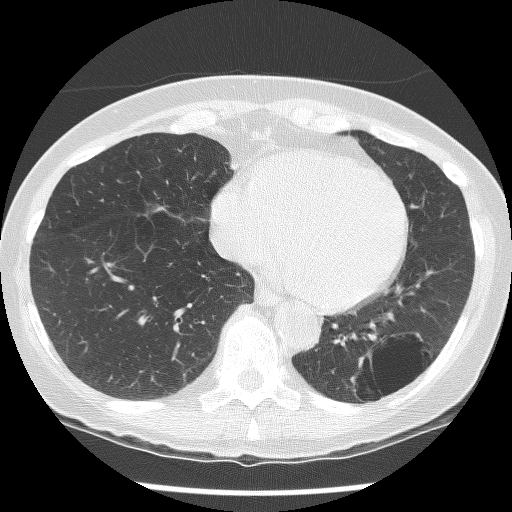
Axial slice from a low-dose chest CT screening exam, second screening round (one year after baseline), lung window (W 1500 / L -600 HU), 2.5 mm slice thickness, lung (sharp) reconstruction kernel (BONE), slice 90 of 136 in the series. Female participant, aged 61 years at enrolment.
Lesion marked by an expert reader, bounding box (x1, y1, x2, y2) in pixels: (332, 327, 436, 417). The screening reader recorded 2 non-calcified nodules or masses ≥4 mm on this exam (left lower lobe, left lower lobe); which of them this box marks is not recorded. Participant outcome: lung cancer diagnosed 585 days after this screen — non-small cell carcinoma, left lower lobe, poorly differentiated (G3), stage IB (AJCC 6th edition), 100 mm at pathology.